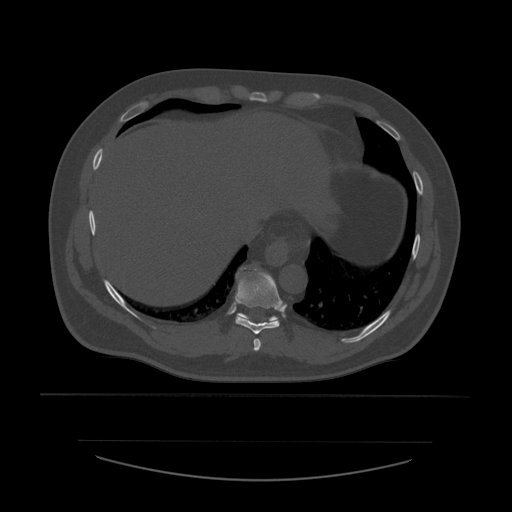
CT including the spine, one axial slice; reconstruction kernel STANDARD; 120 kVp; bone window (W 1800 / L 400 HU); 1.25 mm slice thickness; 512 × 512 image matrix, field of view 441 × 441 mm. Patient age 44 years. Case-level facts recorded for this patient, not image findings: primary cancer: soft tissue sarcoma.
Annotated regions visible in this slice (semi-automatic segmentation, software-assisted and operator-edited):
- T10 vertebra: box from (x=237, y=313) to (x=278, y=321) px
- T8 vertebra: (x=254, y=339)–(x=261, y=353)
- T9 vertebra: (x=235, y=268)–(x=283, y=335)